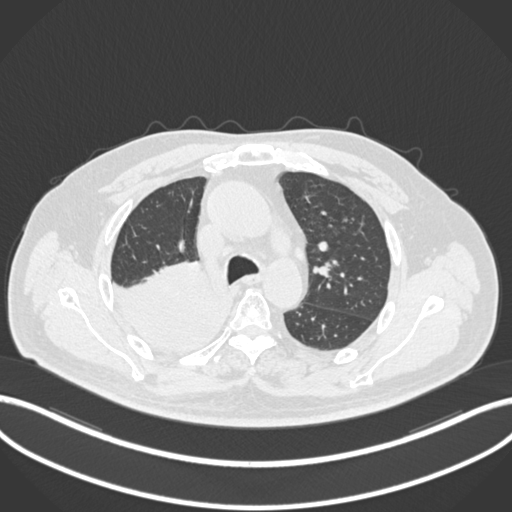
Chest CT, one axial slice. Position 140 of 218 along the scan axis. Reconstruction kernel B30f. 120 kVp. Lung window (W 1500 / L -600 HU). 512 × 512 image matrix, field of view 400 × 400 mm. Male patient, age 68 years. Case-level facts recorded for this patient, not image findings: clinical TNM (as recorded): T2a N0 M0.
Structures marked on this image (bounding box drawn by a radiologist):
- lung tumour (recorded histology: adenocarcinoma): bounding box <114,261,235,355> (left, top, right, bottom; pixels)